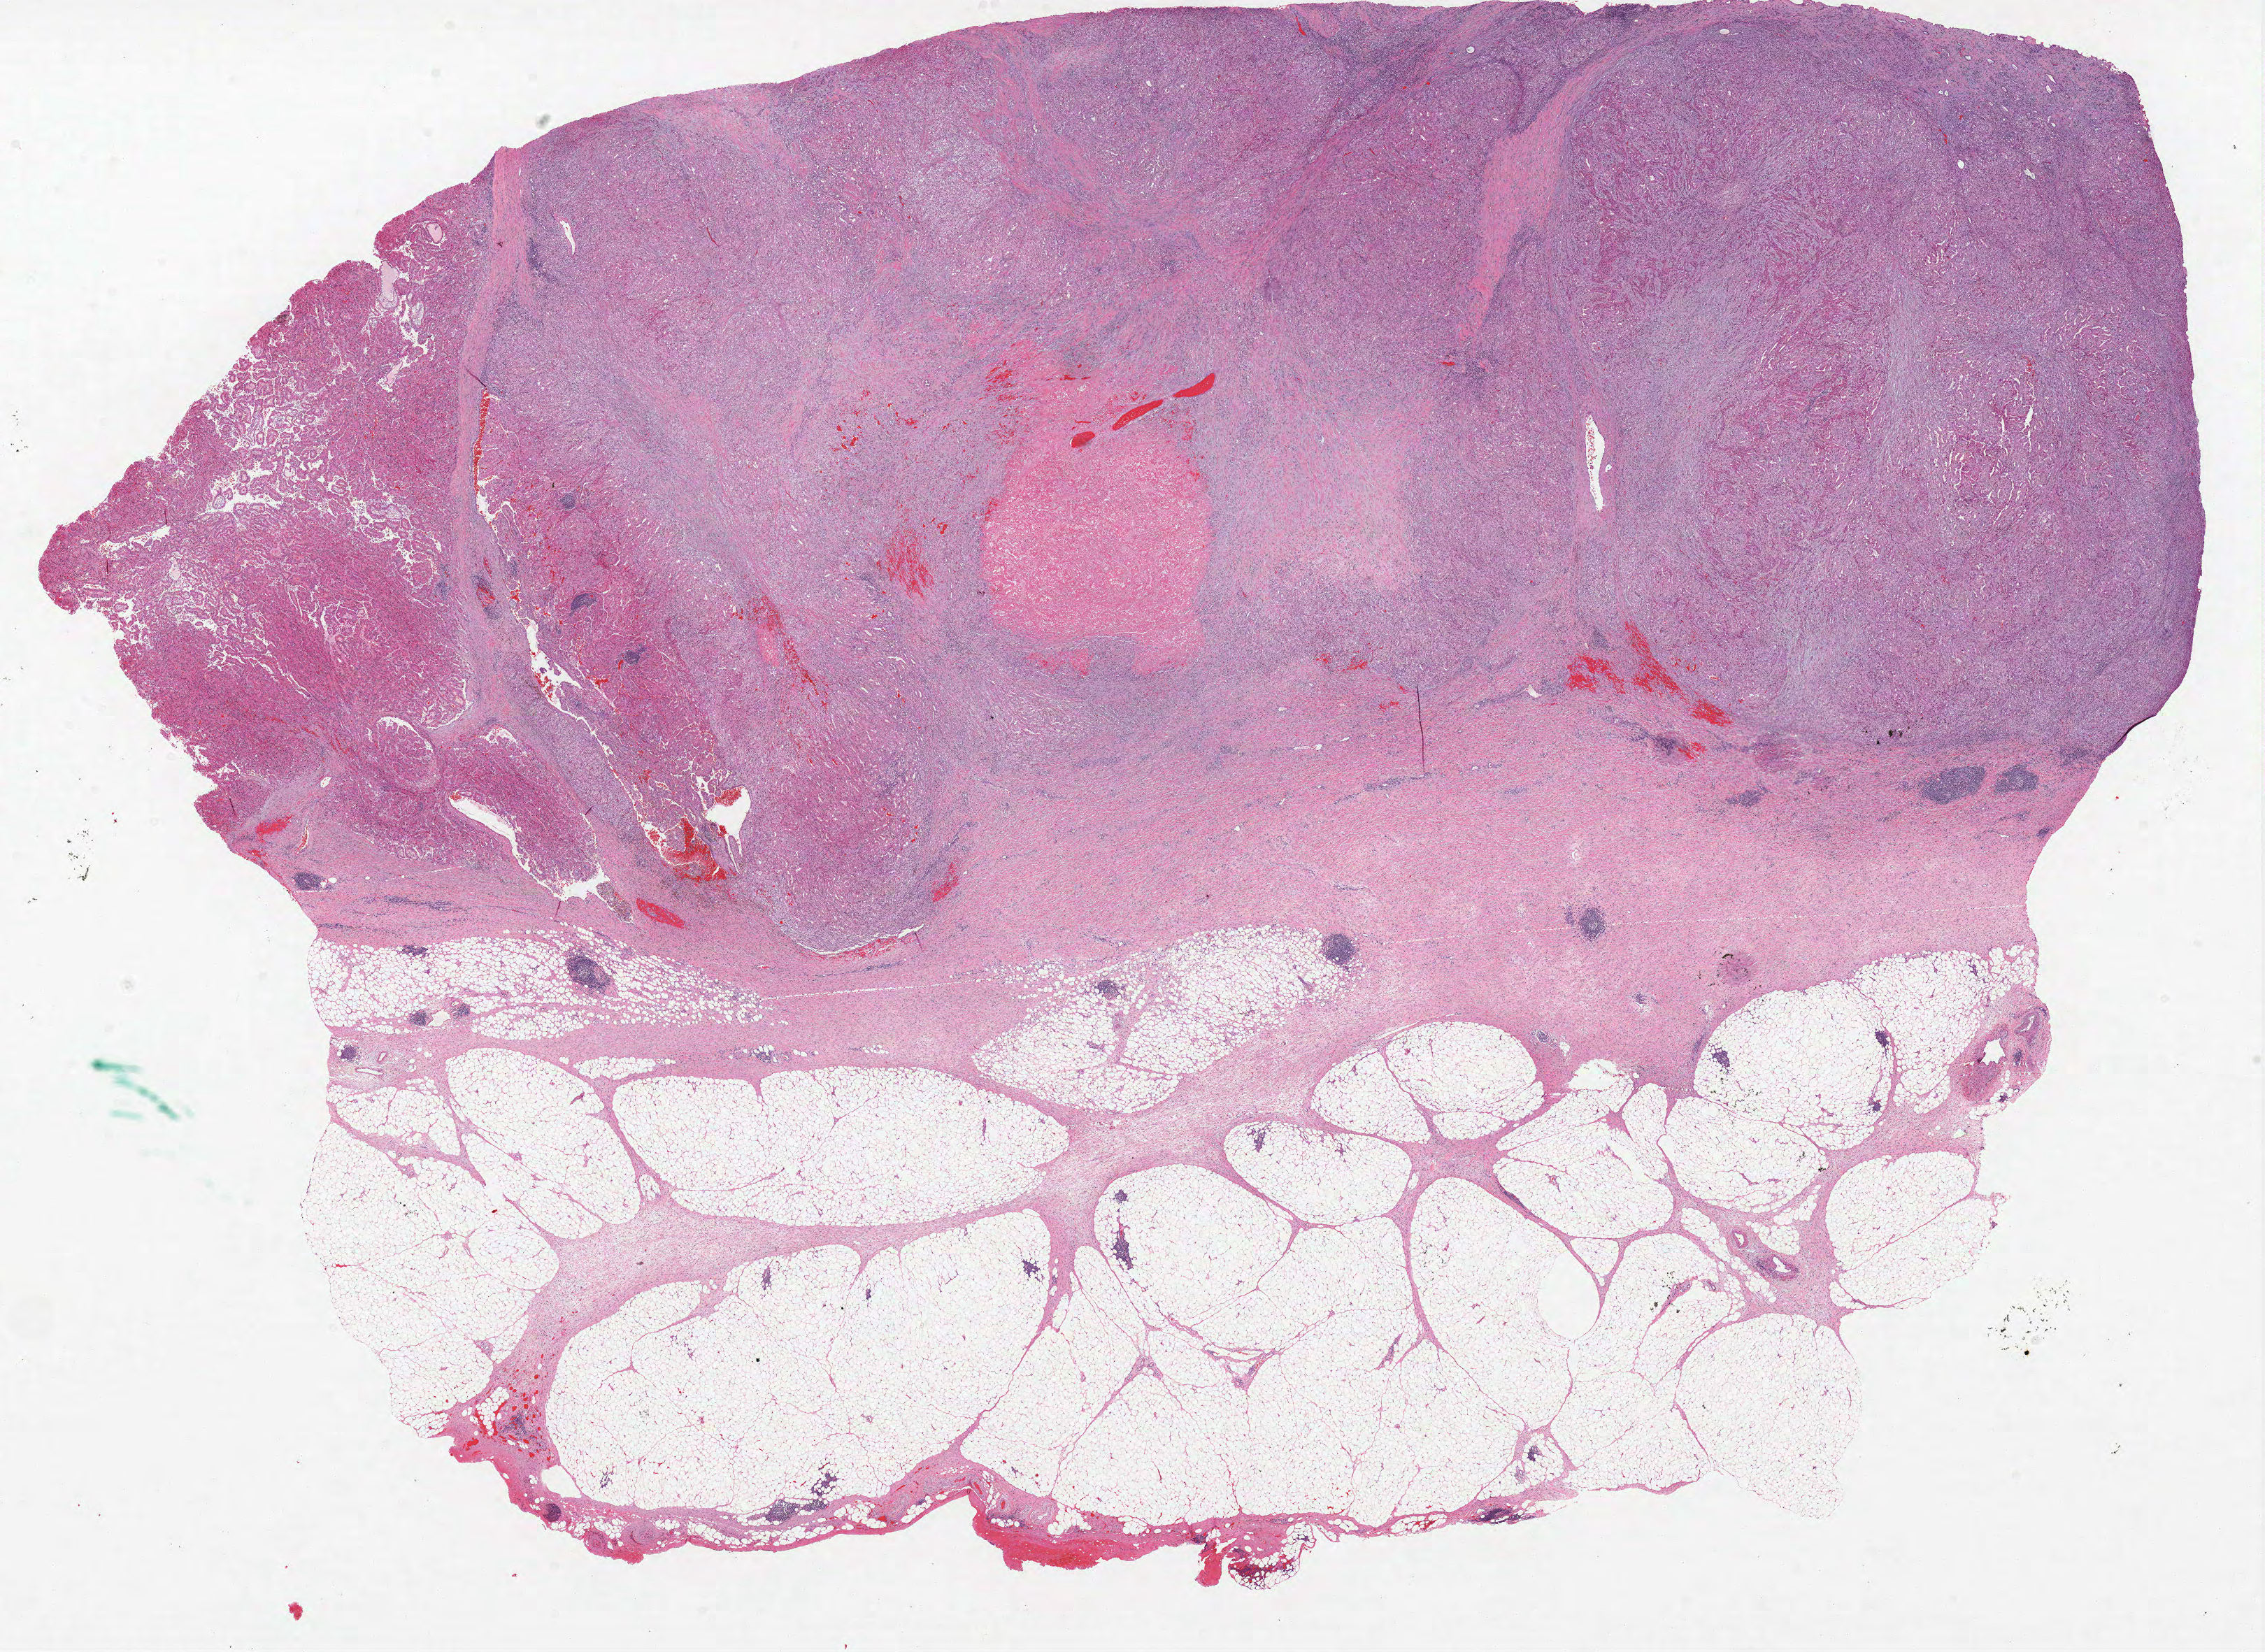
Whole-slide histology image, H&E-stained, shown as a low-resolution overview of the whole scanned area (about 25.9 x 18.9 mm); formalin-fixed paraffin-embedded (FFPE) diagnostic section; primary tumour sample from the kidney. Patient: male, age at initial diagnosis 81 years.
Histologic diagnosis: Papillary adenocarcinoma, NOS. Lymph nodes positive (case pathology): 3 of 8 examined. AJCC pathologic stage: III.